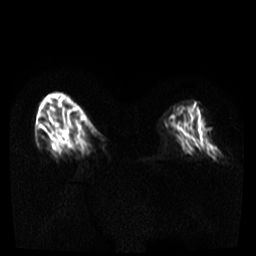
Breast MRI, one axial slice. Slice 11 of 36 in the series (ordered by position). Diffusion-weighted series; image 2 of 4 stored at this slice position (different b-values; order by instance number). 3 T. 5 mm slice thickness. 256 × 256 image matrix, field of view 300 × 300 mm. Female patient.
Structures marked on this image (manually delineated by an expert):
- tumour on diffusion-weighted imaging: bounding box [x1, y1, x2, y2] px = [57, 127, 63, 134]